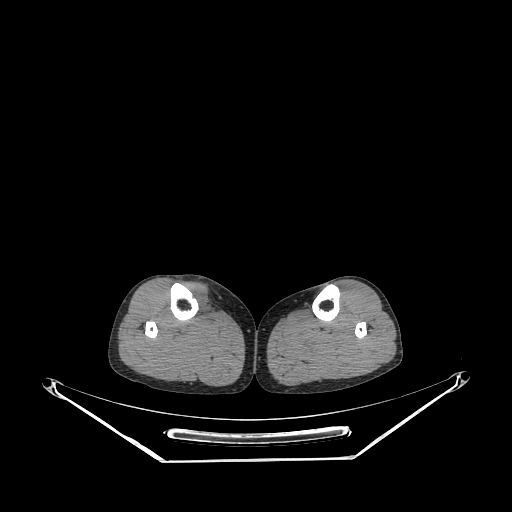
CT of an extremity soft-tissue mass (from a PET/CT study), one axial slice. Reconstruction kernel STANDARD. 140 kVp. Soft-tissue window (W 400 / L 40 HU). 3.75 mm slice thickness. 512 × 512 image matrix. Female patient. From the clinical record (not read from this slice): histological type: undifferentiated – high grade; grade: high; site of the primary tumour: right thigh.
Outlined on this slice (expert contour drawn on MRI and transferred to this co-registered scan by the dataset authors):
- gross tumour volume (mass): box from (x=185, y=283) to (x=209, y=314) px